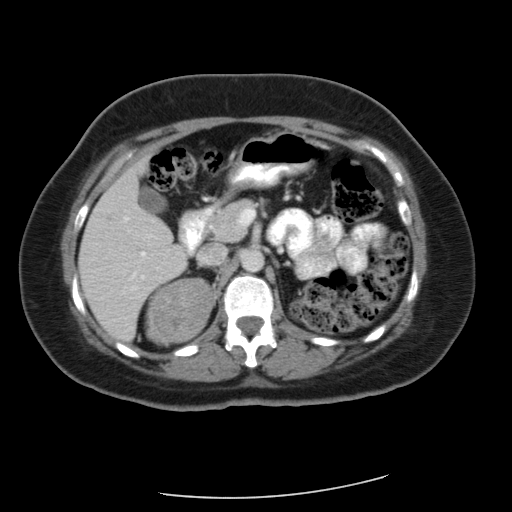
Contrast-enhanced abdominal CT, one axial slice; position 34 of 56 along the scan axis; reconstruction kernel FC12; soft-tissue window (W 400 / L 40 HU); 5 mm slice thickness; 512 × 512 image matrix. Female patient, age 58 years. From the clinical record (not read from this slice): diagnosis: adrenocortical carcinoma; tumour side: right adrenal; tumour size at pathology: 9 cm; Ki-67 index: 25 %; stage (as recorded): 3.
Structures marked on this image (semi-automatically segmented with operator editing):
- mass: bounding box <148,280,213,344> (left, top, right, bottom; pixels)